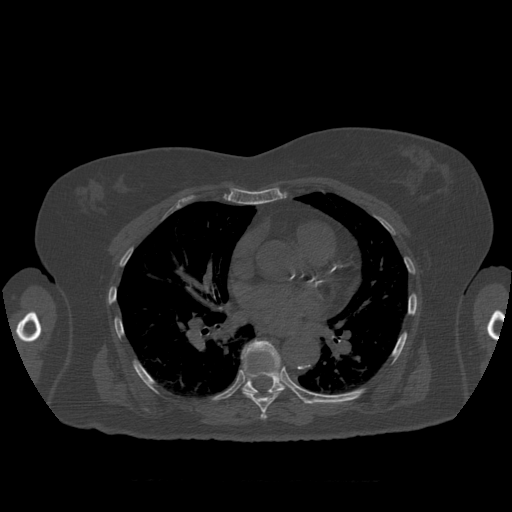
CT including the spine, one axial slice. Position 389 of 399 along the scan axis. Reconstruction kernel STANDARD. Bone window (W 1800 / L 400 HU). 1.25 mm slice thickness. 512 × 512 image matrix, field of view 404 × 404 mm. Patient age 81 years. Case-level facts recorded for this patient, not image findings: primary cancer: renal; vertebrae with lytic lesions (as recorded): L1.
Annotated regions visible in this slice (semi-automatic segmentation, software-assisted and operator-edited):
- T7 vertebra: bounding box (x1, y1, x2, y2) in pixels: (243, 341, 281, 420)
- T8 vertebra: (242, 340, 302, 400)